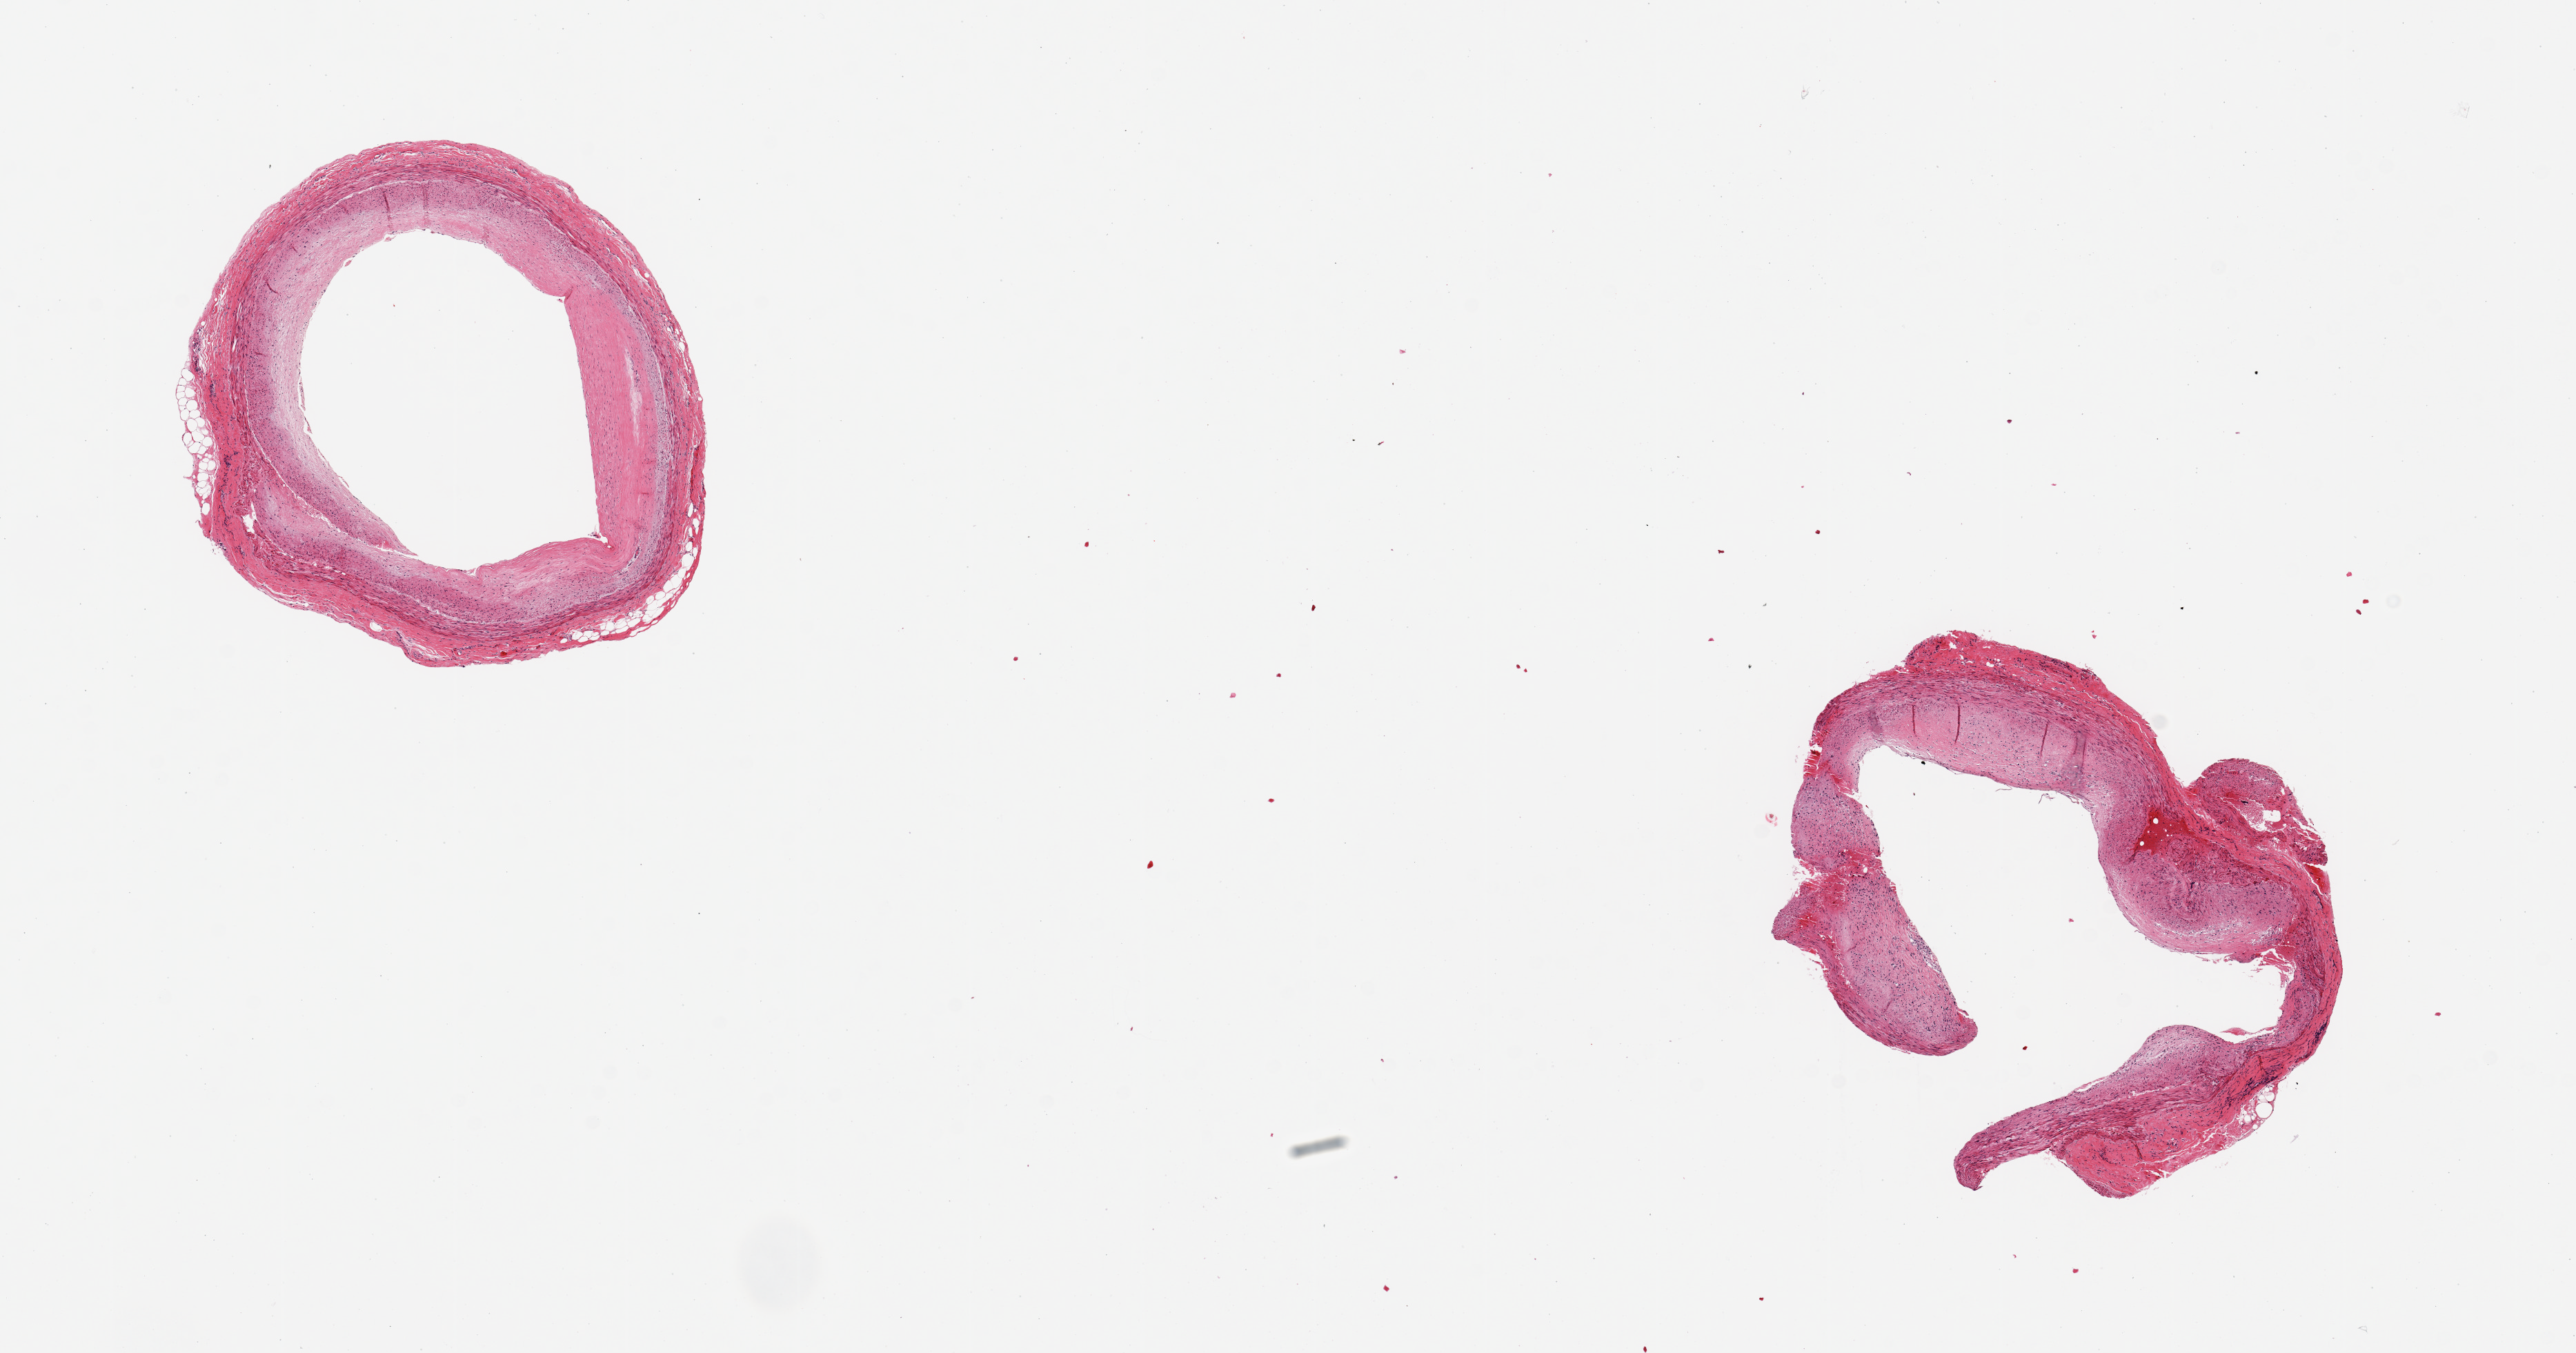
Whole-slide image, hematoxylin and eosin (H&E) stain, a low-resolution overview of the entire scanned area, about 14.8 x 7.8 mm (acquisition: 20x scan); PAXgene-fixed paraffin-embedded (PFPE) section; sampled site (target tissue): coronary artery; donor tissue sample. Donor: female.
Reviewer comment on this tissue sample: 2 pieces; well trimmed; focal plaques.